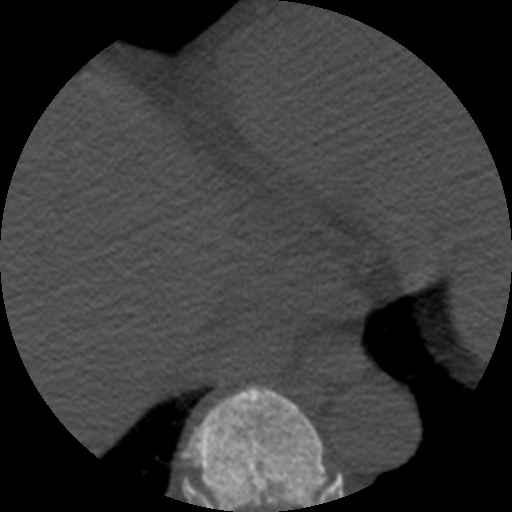
CT including the spine, one axial slice; position 303 of 508 along the scan axis; reconstruction kernel STANDARD; bone window (W 1800 / L 400 HU); 1.25 mm slice thickness; 512 × 512 image matrix. Patient age 57 years. From the clinical record (not read from this slice): primary cancer: prostate.
Annotated regions visible in this slice (semi-automatic segmentation, software-assisted and operator-edited):
- T8 vertebra: bounding box (x1, y1, x2, y2) in pixels: (183, 386, 328, 512)
- T9 vertebra: (323, 465, 326, 469)